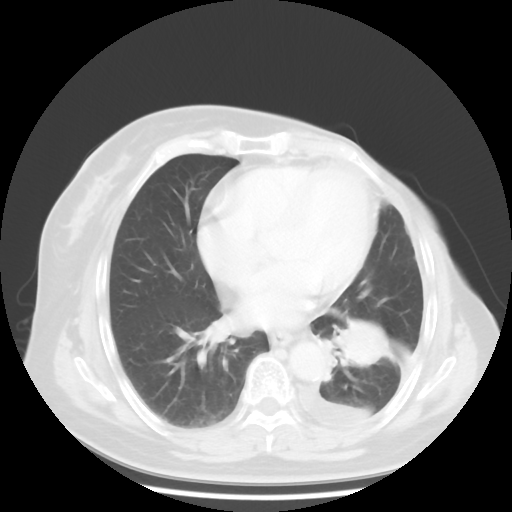
Chest CT, one axial slice. Lung window (W 1500 / L -600 HU). 5 mm slice thickness. 512 × 512 image matrix, field of view 360 × 360 mm. Patient: female, 63 years. From the clinical record (not read from this slice): clinical TNM (as recorded): T2 N0 M1.
Outlined on this slice (bounding box drawn by a radiologist):
- lung tumour (recorded histology: adenocarcinoma): bounding box (x1, y1, x2, y2) in pixels: (331, 312, 400, 387)